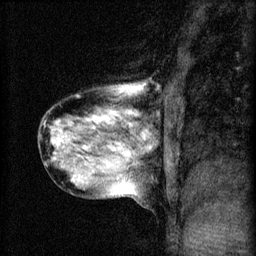
Breast MRI (dynamic contrast-enhanced), one sagittal slice. Position 24 of 60 along the scan axis. 3 images stored at this slice position (order not interpretable as contrast timing). 1.5 T. TE 4.2 ms, TR 8.2 ms. 2 mm slice thickness. 256 × 256 image matrix, field of view 180 × 180 mm. Female patient, age 40 years.
Annotated regions visible in this slice (semi-automatic segmentation, software-assisted and operator-edited):
- analysis volume of interest (the breast-tissue region the enhancement analysis was run in; not a lesion): box from (x=37, y=80) to (x=165, y=207) px
- tumour enhancement mask (voxels above the 70 % enhancement threshold inside the analysis volume of interest): (x=57, y=86)–(x=149, y=181)